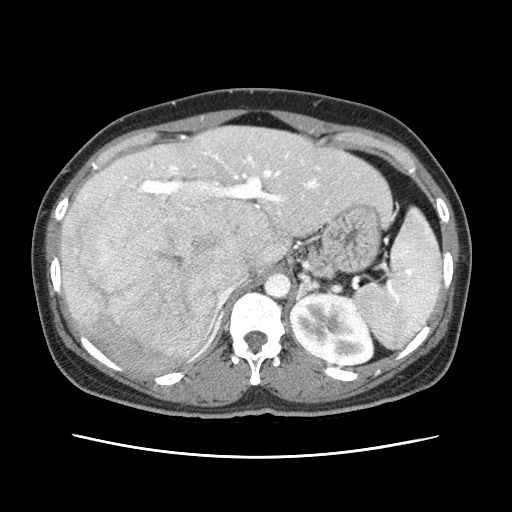
Contrast-enhanced abdominal CT (liver protocol), one axial slice. Position 40 of 79 along the scan axis. Reconstruction kernel STANDARD. Soft-tissue window (W 400 / L 40 HU). 512 × 512 image matrix, field of view 340 × 340 mm. Case-level facts recorded for this patient, not image findings: diagnosis: hepatocellular carcinoma (patient treated with transarterial chemoembolisation; whether this scan precedes or follows treatment is not stated here); TNM stage (as recorded): Stage-I; Child-Pugh class: A.
Outlined on this slice (semi-automatically segmented with operator editing):
- abdominal aorta: bounding box [x1, y1, x2, y2] px = [265, 272, 291, 298]
- liver parenchyma outside the tumour (the mass and vessels are separate outlines, so this box may not span the whole liver): [60, 126, 390, 368]
- mass: [68, 189, 267, 362]
- liver vessels: [85, 153, 319, 342]